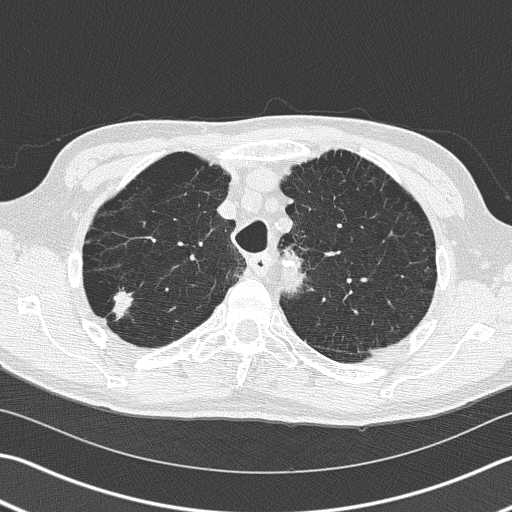
Chest CT (low-dose screening protocol), one axial image. Baseline annual screen. Lung window (W 1500 / L -600 HU). Lung (sharp) reconstruction kernel (B50f). 512 × 512 image matrix, field of view 346 × 346 mm. Male participant, aged 66 years at enrolment. Current smoker at enrolment.
Expert-annotated lung lesion, bounding box (x1, y1, x2, y2) in pixels: (86, 270, 145, 339). Screening reader's record for this exam (one nodule recorded; not confirmed to be the boxed lesion): non-calcified nodule or mass ≥4 mm, right upper lobe, 39 × 23 mm, spiculated (stellate) margins, soft tissue attenuation. Later outcome: lung cancer diagnosed 36 days after this screen — squamous cell carcinoma, NOS, right upper lobe, poorly differentiated (G3), stage IB (AJCC 6th edition), 23 mm at pathology.